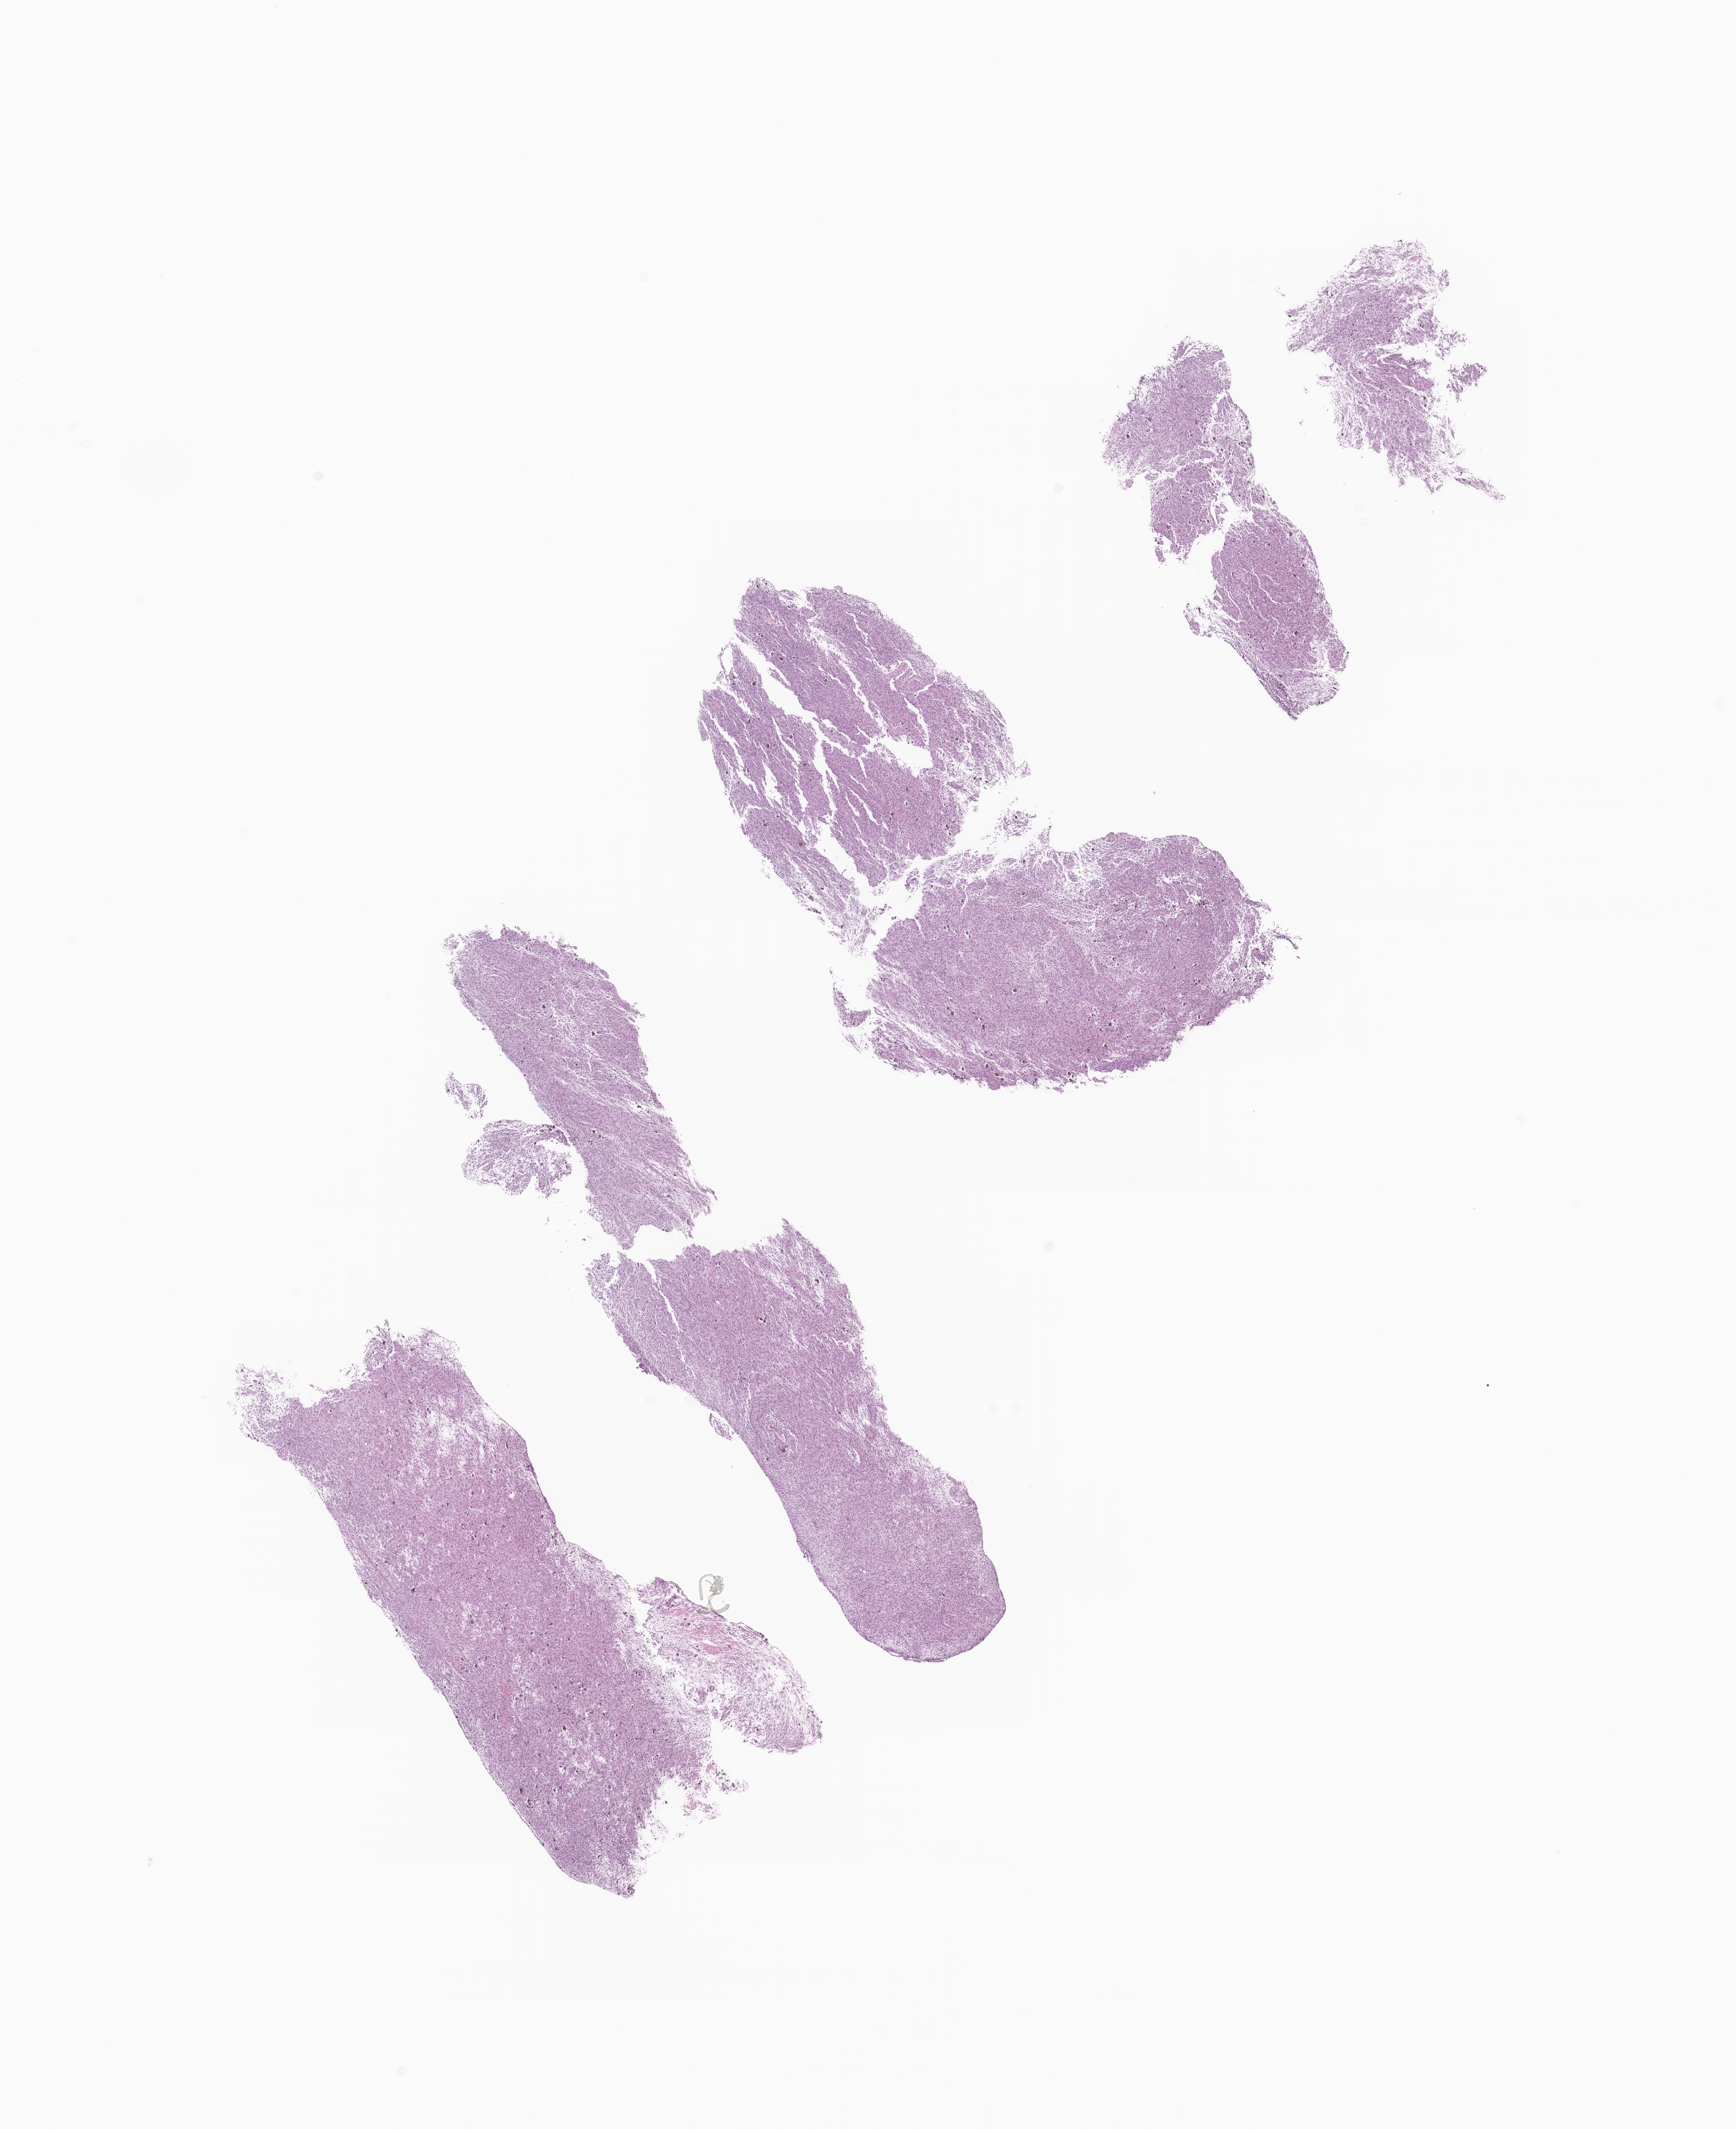
Whole-slide image, hematoxylin and eosin (H&E) stain of tumor tissue from the brain, shown as a low-resolution overview of the whole scanned area (about 13.8 x 16.9 mm), formalin-fixed, paraffin-embedded (FFPE) tissue. Patient female; age 86 months.
Diagnosis: Glioma, malignant.